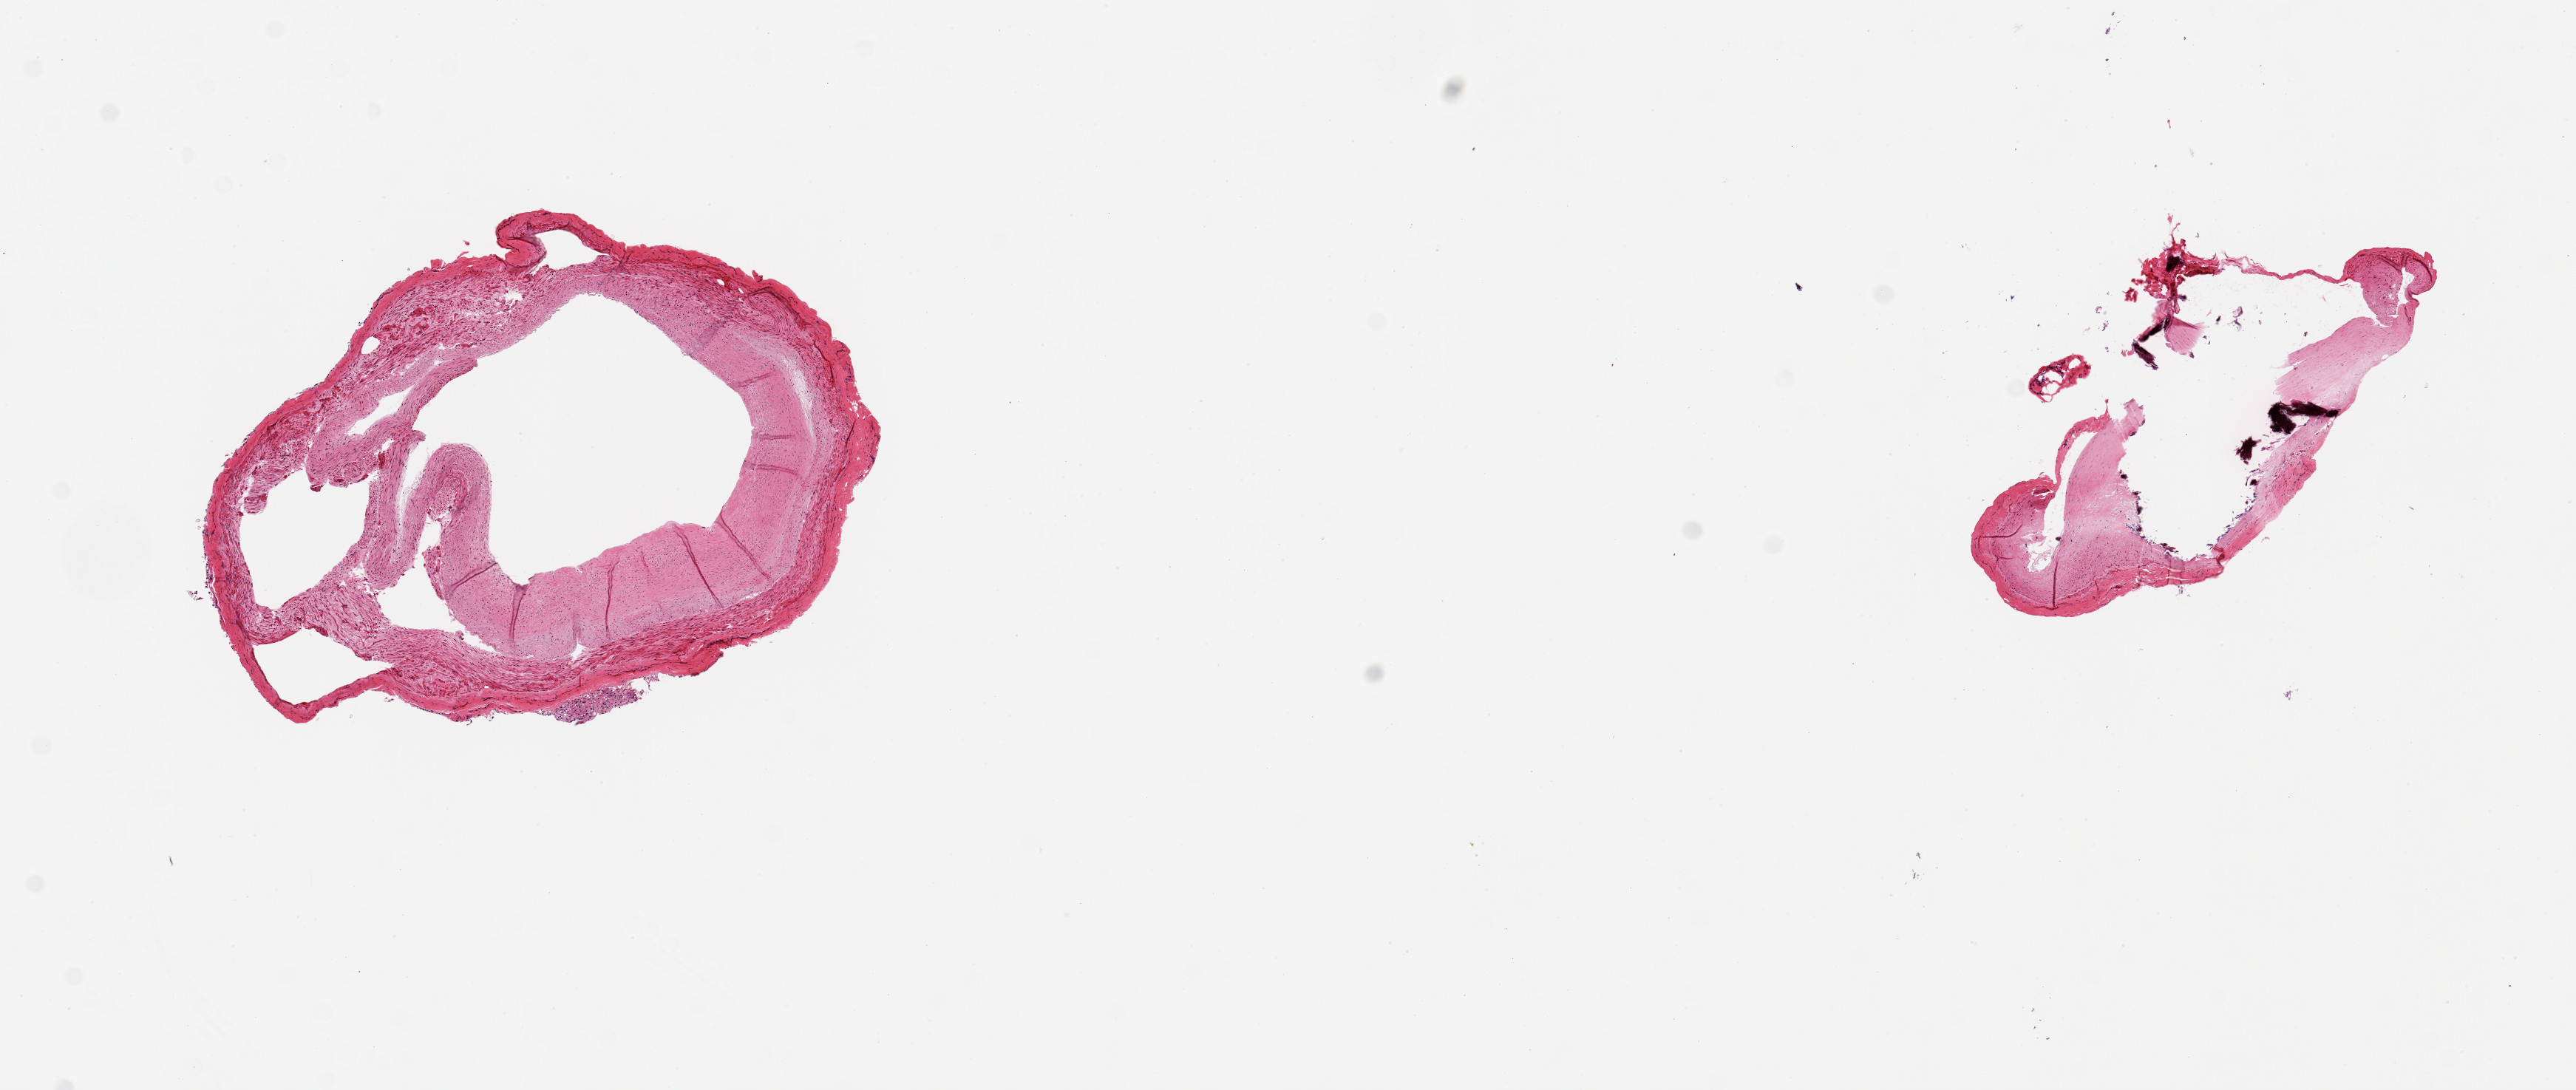
Whole-slide image, H&E stain, brightfield, low-resolution overview of the scanned area, about 13.8 x 5.8 mm (slide scanned at 20x); PAXgene-fixed, paraffin-embedded tissue; sampled site (target tissue): coronary artery; donor tissue sample. Male donor.
Pathologist's review note for this sample: 2 pieces, 4x3 & 3x1.5mm; 1 with fibrocalcific sclerosis; other with uniform fibrous plaque.